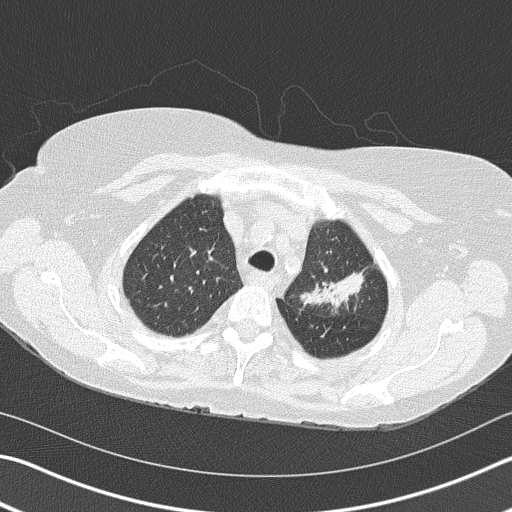
Axial slice from a low-dose chest CT screening exam. Second annual screen. Lung window (W 1500 / L -600 HU). 2 mm slice thickness. Lung (sharp) reconstruction kernel (B50f). Female participant, aged 68 years at enrolment. Former smoker at enrolment.
• Lesion marked by an expert reader, bounding box [x1, y1, x2, y2] px = [291, 231, 376, 324].
• Screening reader's record for this exam (one nodule recorded; not confirmed to be the boxed lesion): non-calcified nodule or mass ≥4 mm, left upper lobe, 4 × 2 mm, spiculated (stellate) margins, soft tissue attenuation, pre-existing on the prior screen: yes; interval growth: yes.